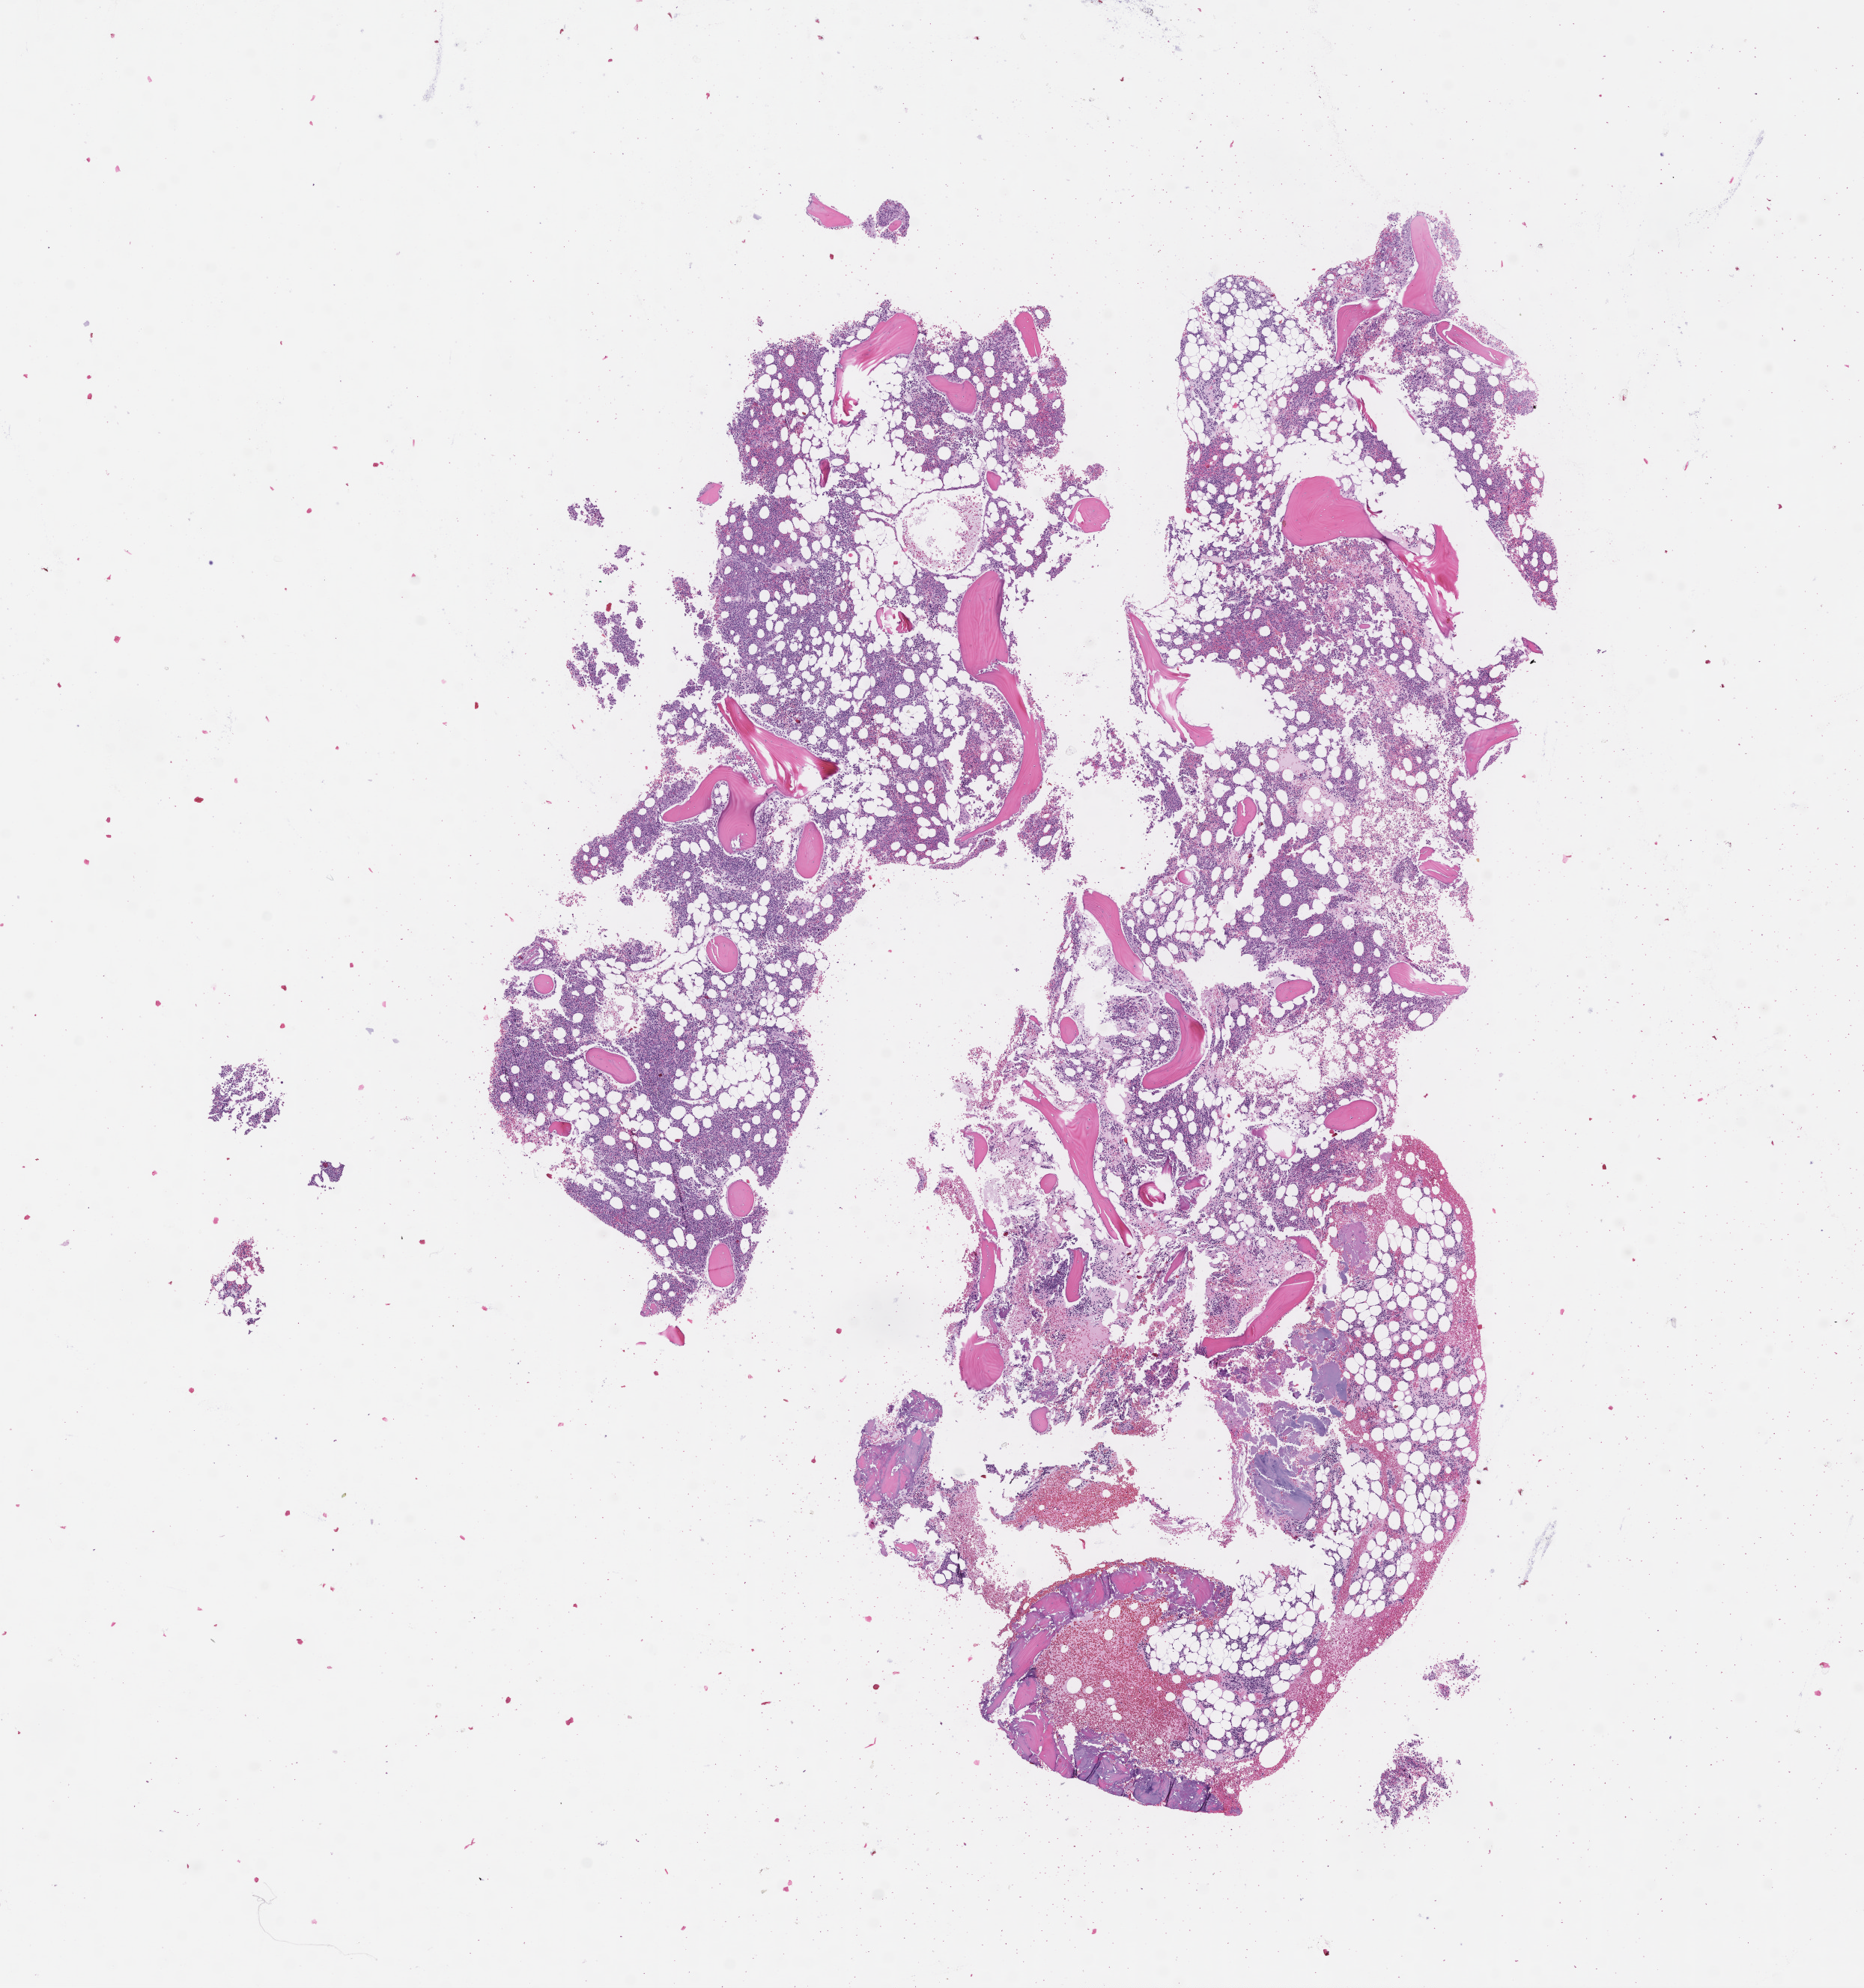
Whole-slide image, hematoxylin and eosin (H&E) stain — low-resolution overview of the scanned area, about 10.1 x 10.7 mm; formalin-fixed, paraffin-embedded (FFPE) tissue; tissue site: bone marrow; specimen time point: archival tissue. Male patient.
* this section: primary tumour tissue
* diagnosis: Plasma Cell Myeloma